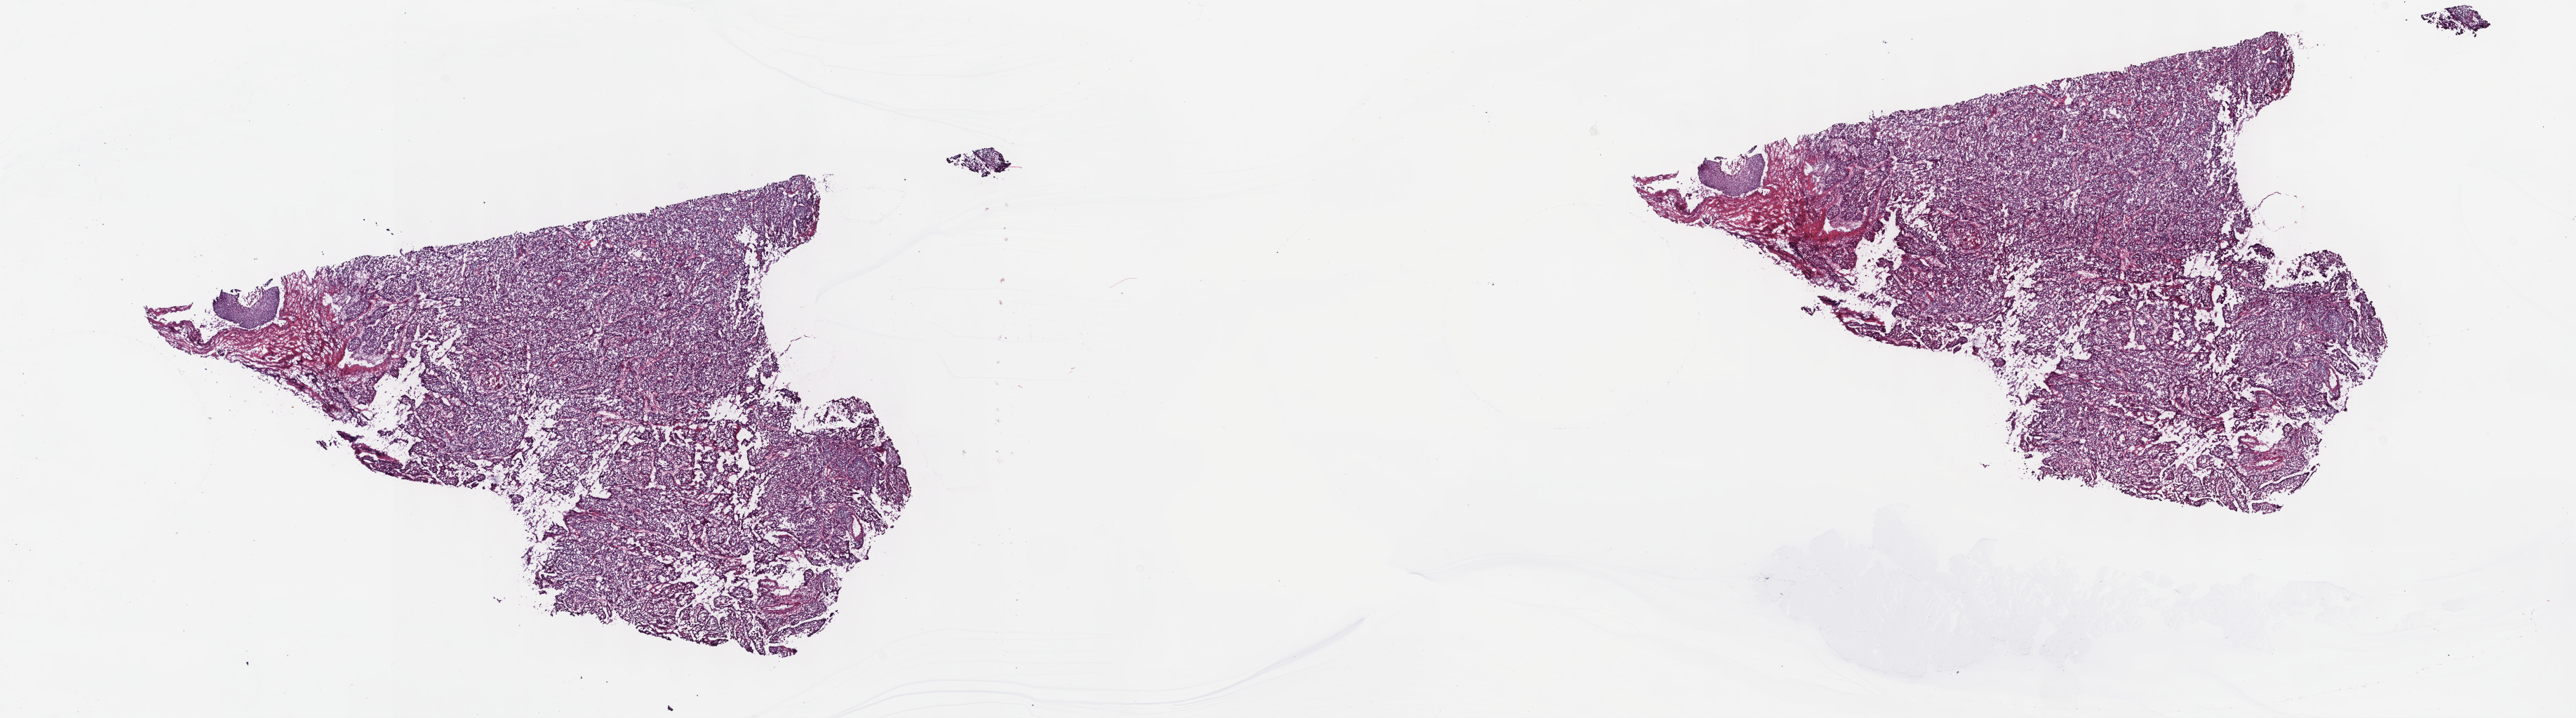
Digitized H&E tissue section (whole slide), a low-resolution overview of the entire scanned area, about 29.7 x 8.3 mm, frozen section from the top of the tissue portion, primary tumour sample from the cervix. Female patient; age at initial diagnosis 38 years. Histologic grade: GX (grade cannot be assessed). Pathologist review of this section (percent, as recorded): tumour cells 80%, tumour nuclei 80%, normal cells 10%, stromal cells 8%, necrosis 2%. Infiltration values recorded for this section: lymphocyte infiltration 2%, monocyte infiltration 0%, neutrophil infiltration 5%.
FIGO stage: I. Pathologic diagnosis: Squamous cell carcinoma, keratinizing, NOS.